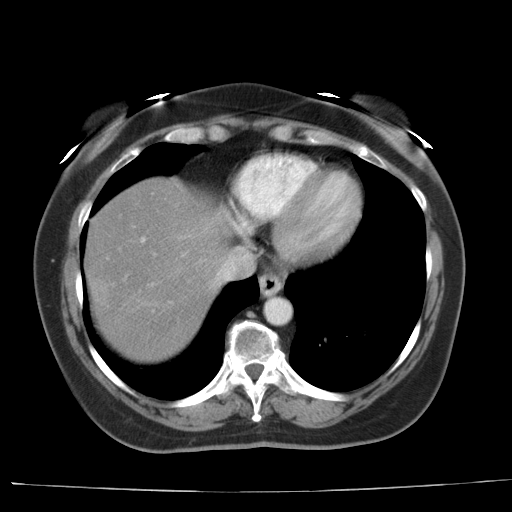
Contrast-enhanced abdominal CT, one axial slice. Position 33 of 44 along the scan axis. Reconstruction kernel AA-1. 140 kVp. Soft-tissue window (W 400 / L 40 HU). 512 × 512 image matrix, field of view 373 × 373 mm. Female patient. From the clinical record (not read from this slice): diagnosis: colorectal cancer liver metastases, imaged before liver resection.
Annotated regions visible in this slice (manually delineated by an expert):
- hepatic veins: box from (x=168, y=247) to (x=254, y=305) px
- liver: (x=86, y=178)–(x=232, y=364)
- planned liver remnant (the part of the liver to remain after resection): (x=119, y=178)–(x=233, y=269)
- portal vein (with intrahepatic branches): (x=140, y=217)–(x=218, y=286)